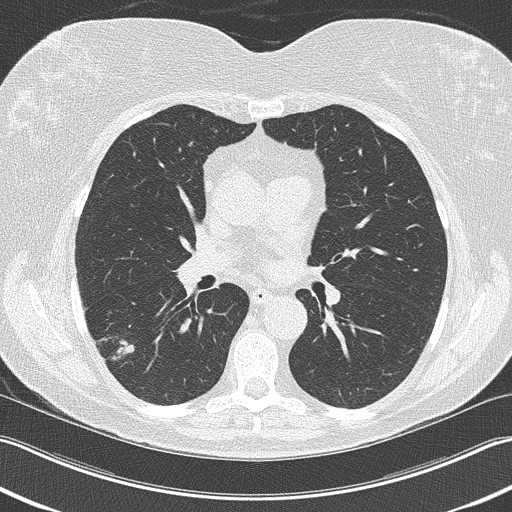
Low-dose screening chest CT, one axial slice; slice 125 of 210 in the series (ordered by position); lung window (W 1500 / L -600 HU); 2 mm slice thickness; 512 × 512 image matrix, field of view 348 × 348 mm.
Outlined on this slice (manually delineated by an expert):
- lesion 1 (tumor, lower lobe of right lung): box from (x=112, y=339) to (x=135, y=360) px